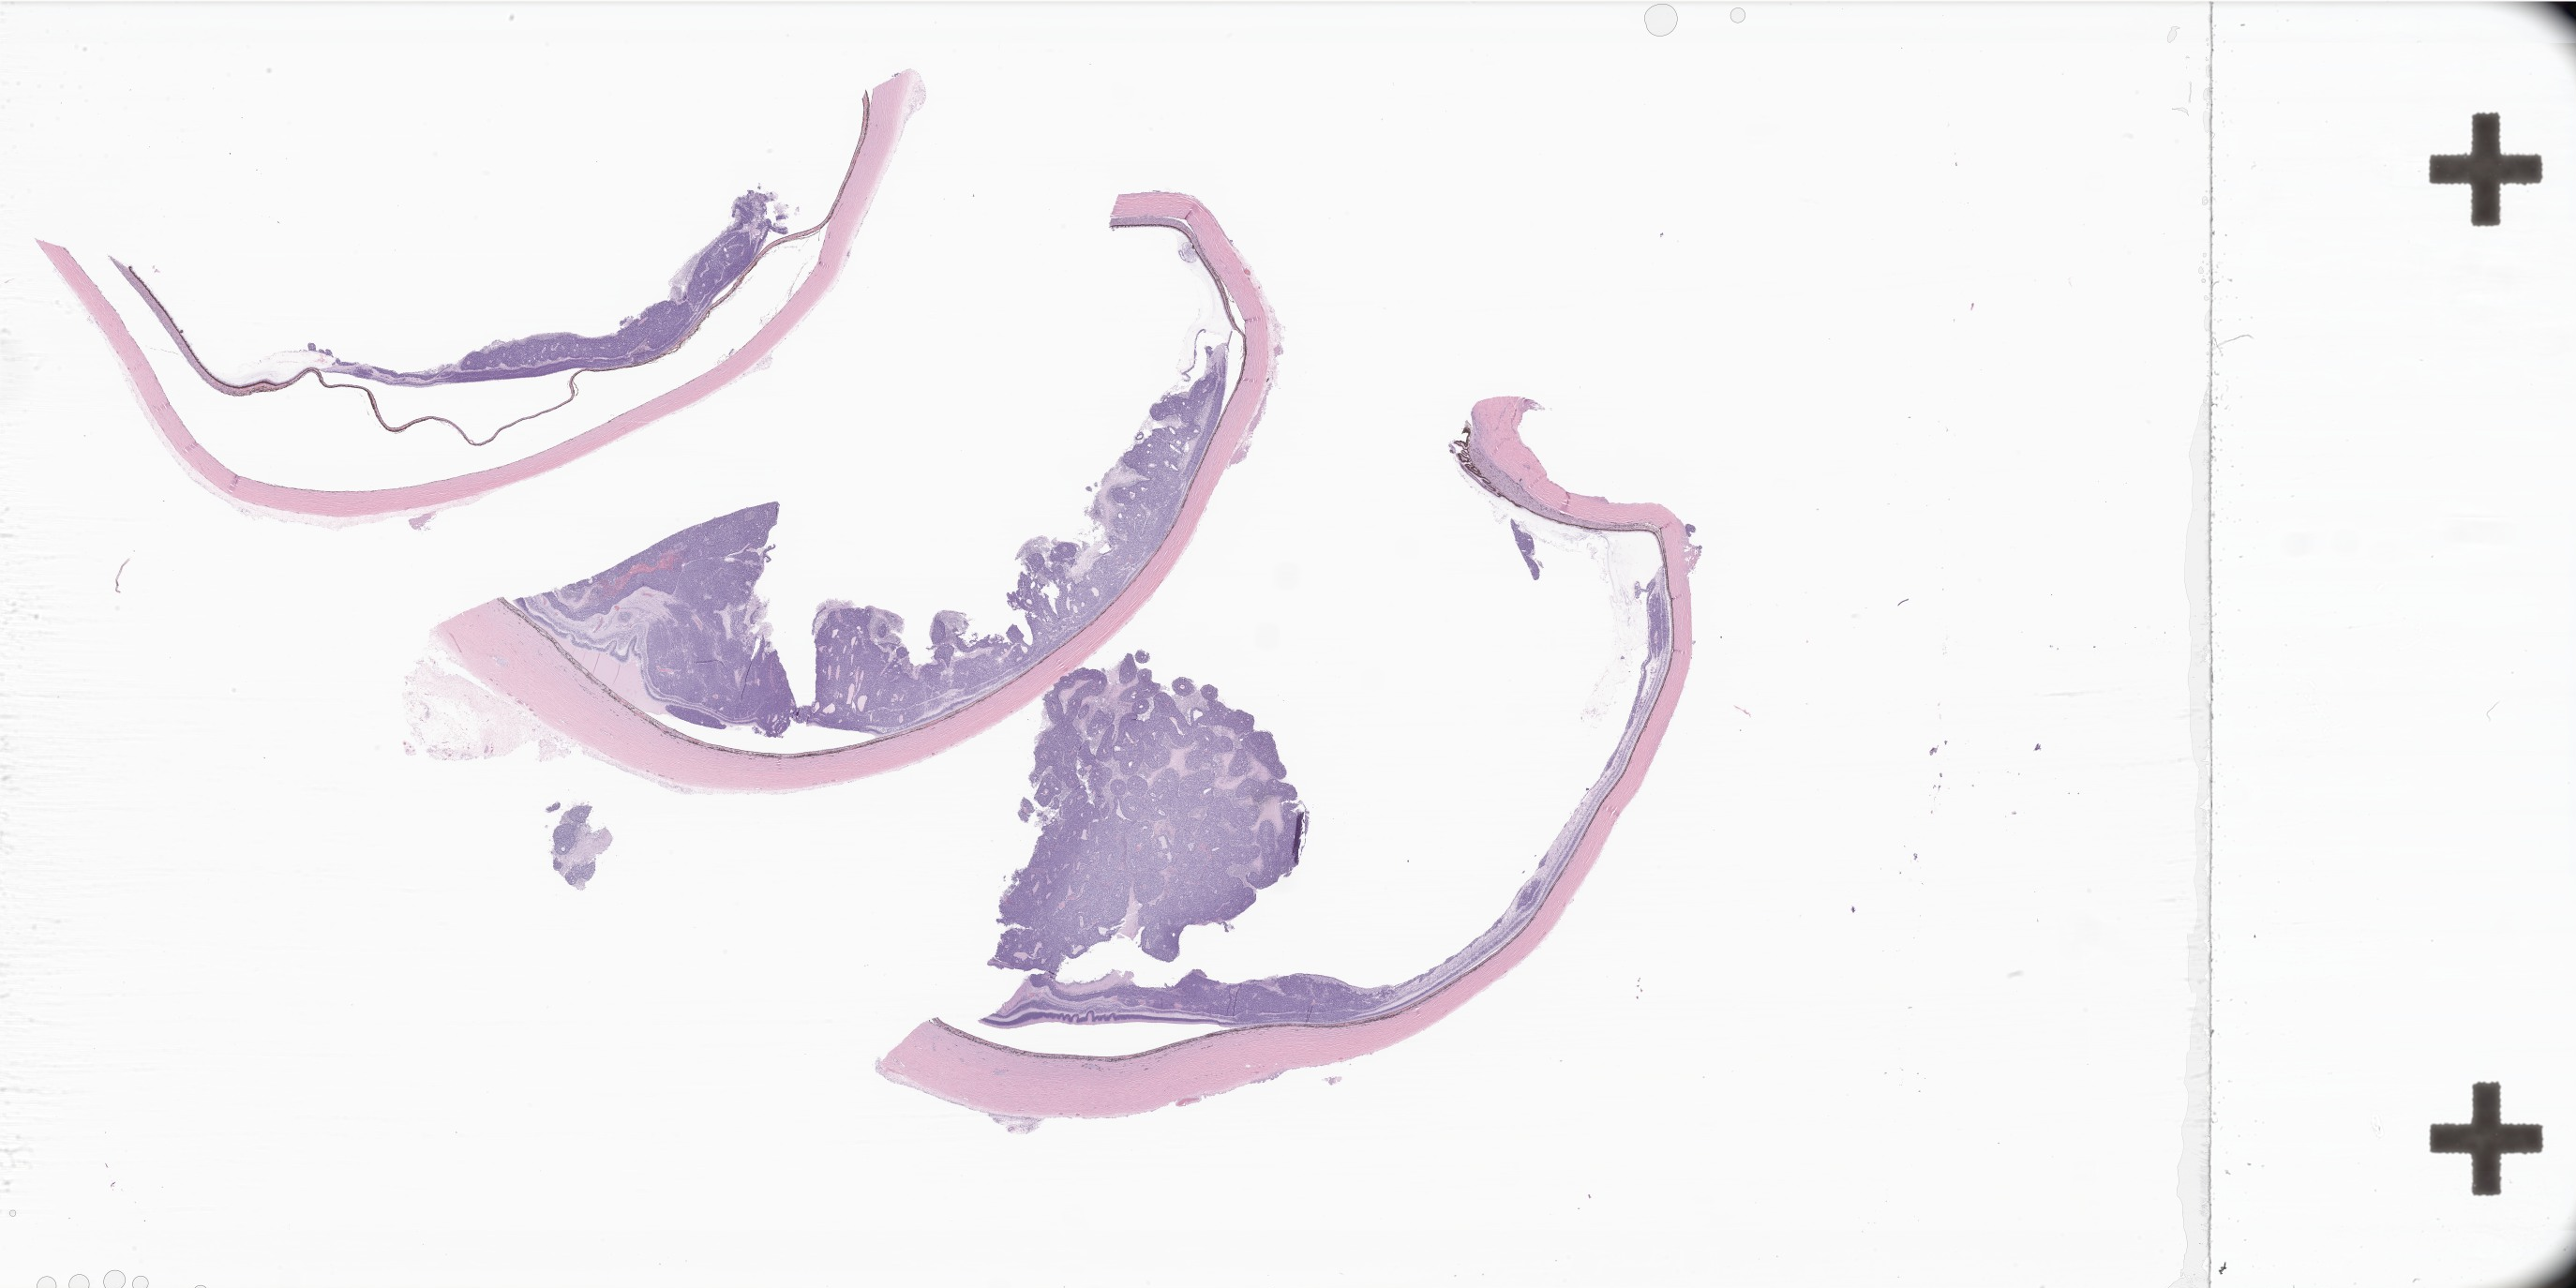
Whole-slide image, hematoxylin and eosin (H&E) stain of tumor tissue from the retina, shown as a low-resolution overview of the whole scanned area (about 46.3 x 23.2 mm), formalin-fixed, paraffin-embedded (FFPE) tissue. Patient female; age 45 months (3 years 9 months).
- diagnosis (ICD-O-3 morphology term): Retinoblastoma, NOS